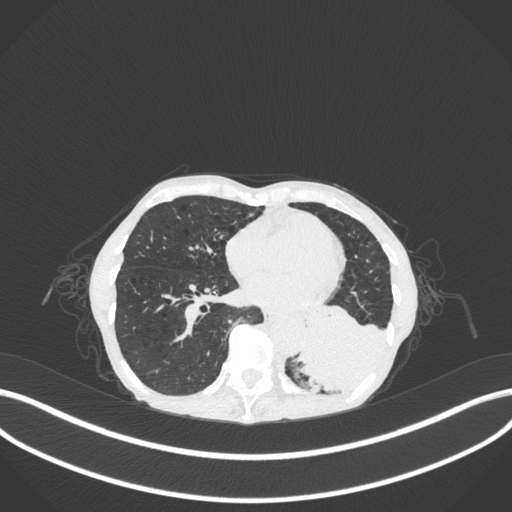
Chest CT, one axial slice. Position 97 of 347 along the scan axis. 120 kVp. Lung window (W 1500 / L -600 HU). 1 mm slice thickness. 512 × 512 image matrix, field of view 400 × 400 mm. Female patient, age 70 years. From the clinical record (not read from this slice): clinical TNM (as recorded): T3 N0 M0.
Annotated regions visible in this slice (rectangle marked by the reading radiologist):
- lung tumour (recorded histology: small cell carcinoma): bounding box (x1, y1, x2, y2) in pixels: (292, 298, 401, 398)